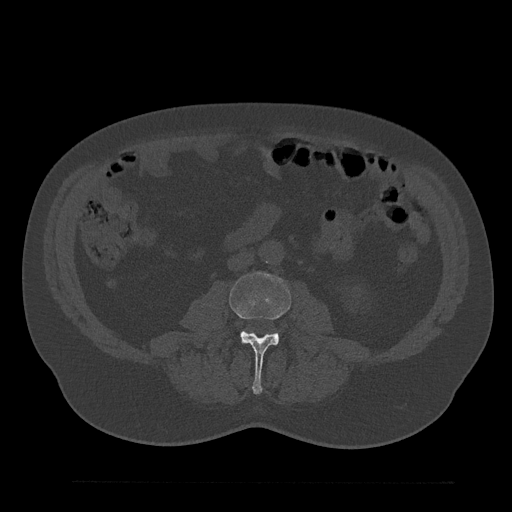
CT including the spine, one axial slice. Position 20 of 797 along the scan axis. 120 kVp. Bone window (W 1800 / L 400 HU). 512 × 512 image matrix, field of view 430 × 430 mm. Male patient, age 61 years. From the clinical record (not read from this slice): primary cancer: prostate.
Structures marked on this image (semi-automatic segmentation, software-assisted and operator-edited):
- L3 vertebra: box from (x=229, y=272) to (x=291, y=395) px